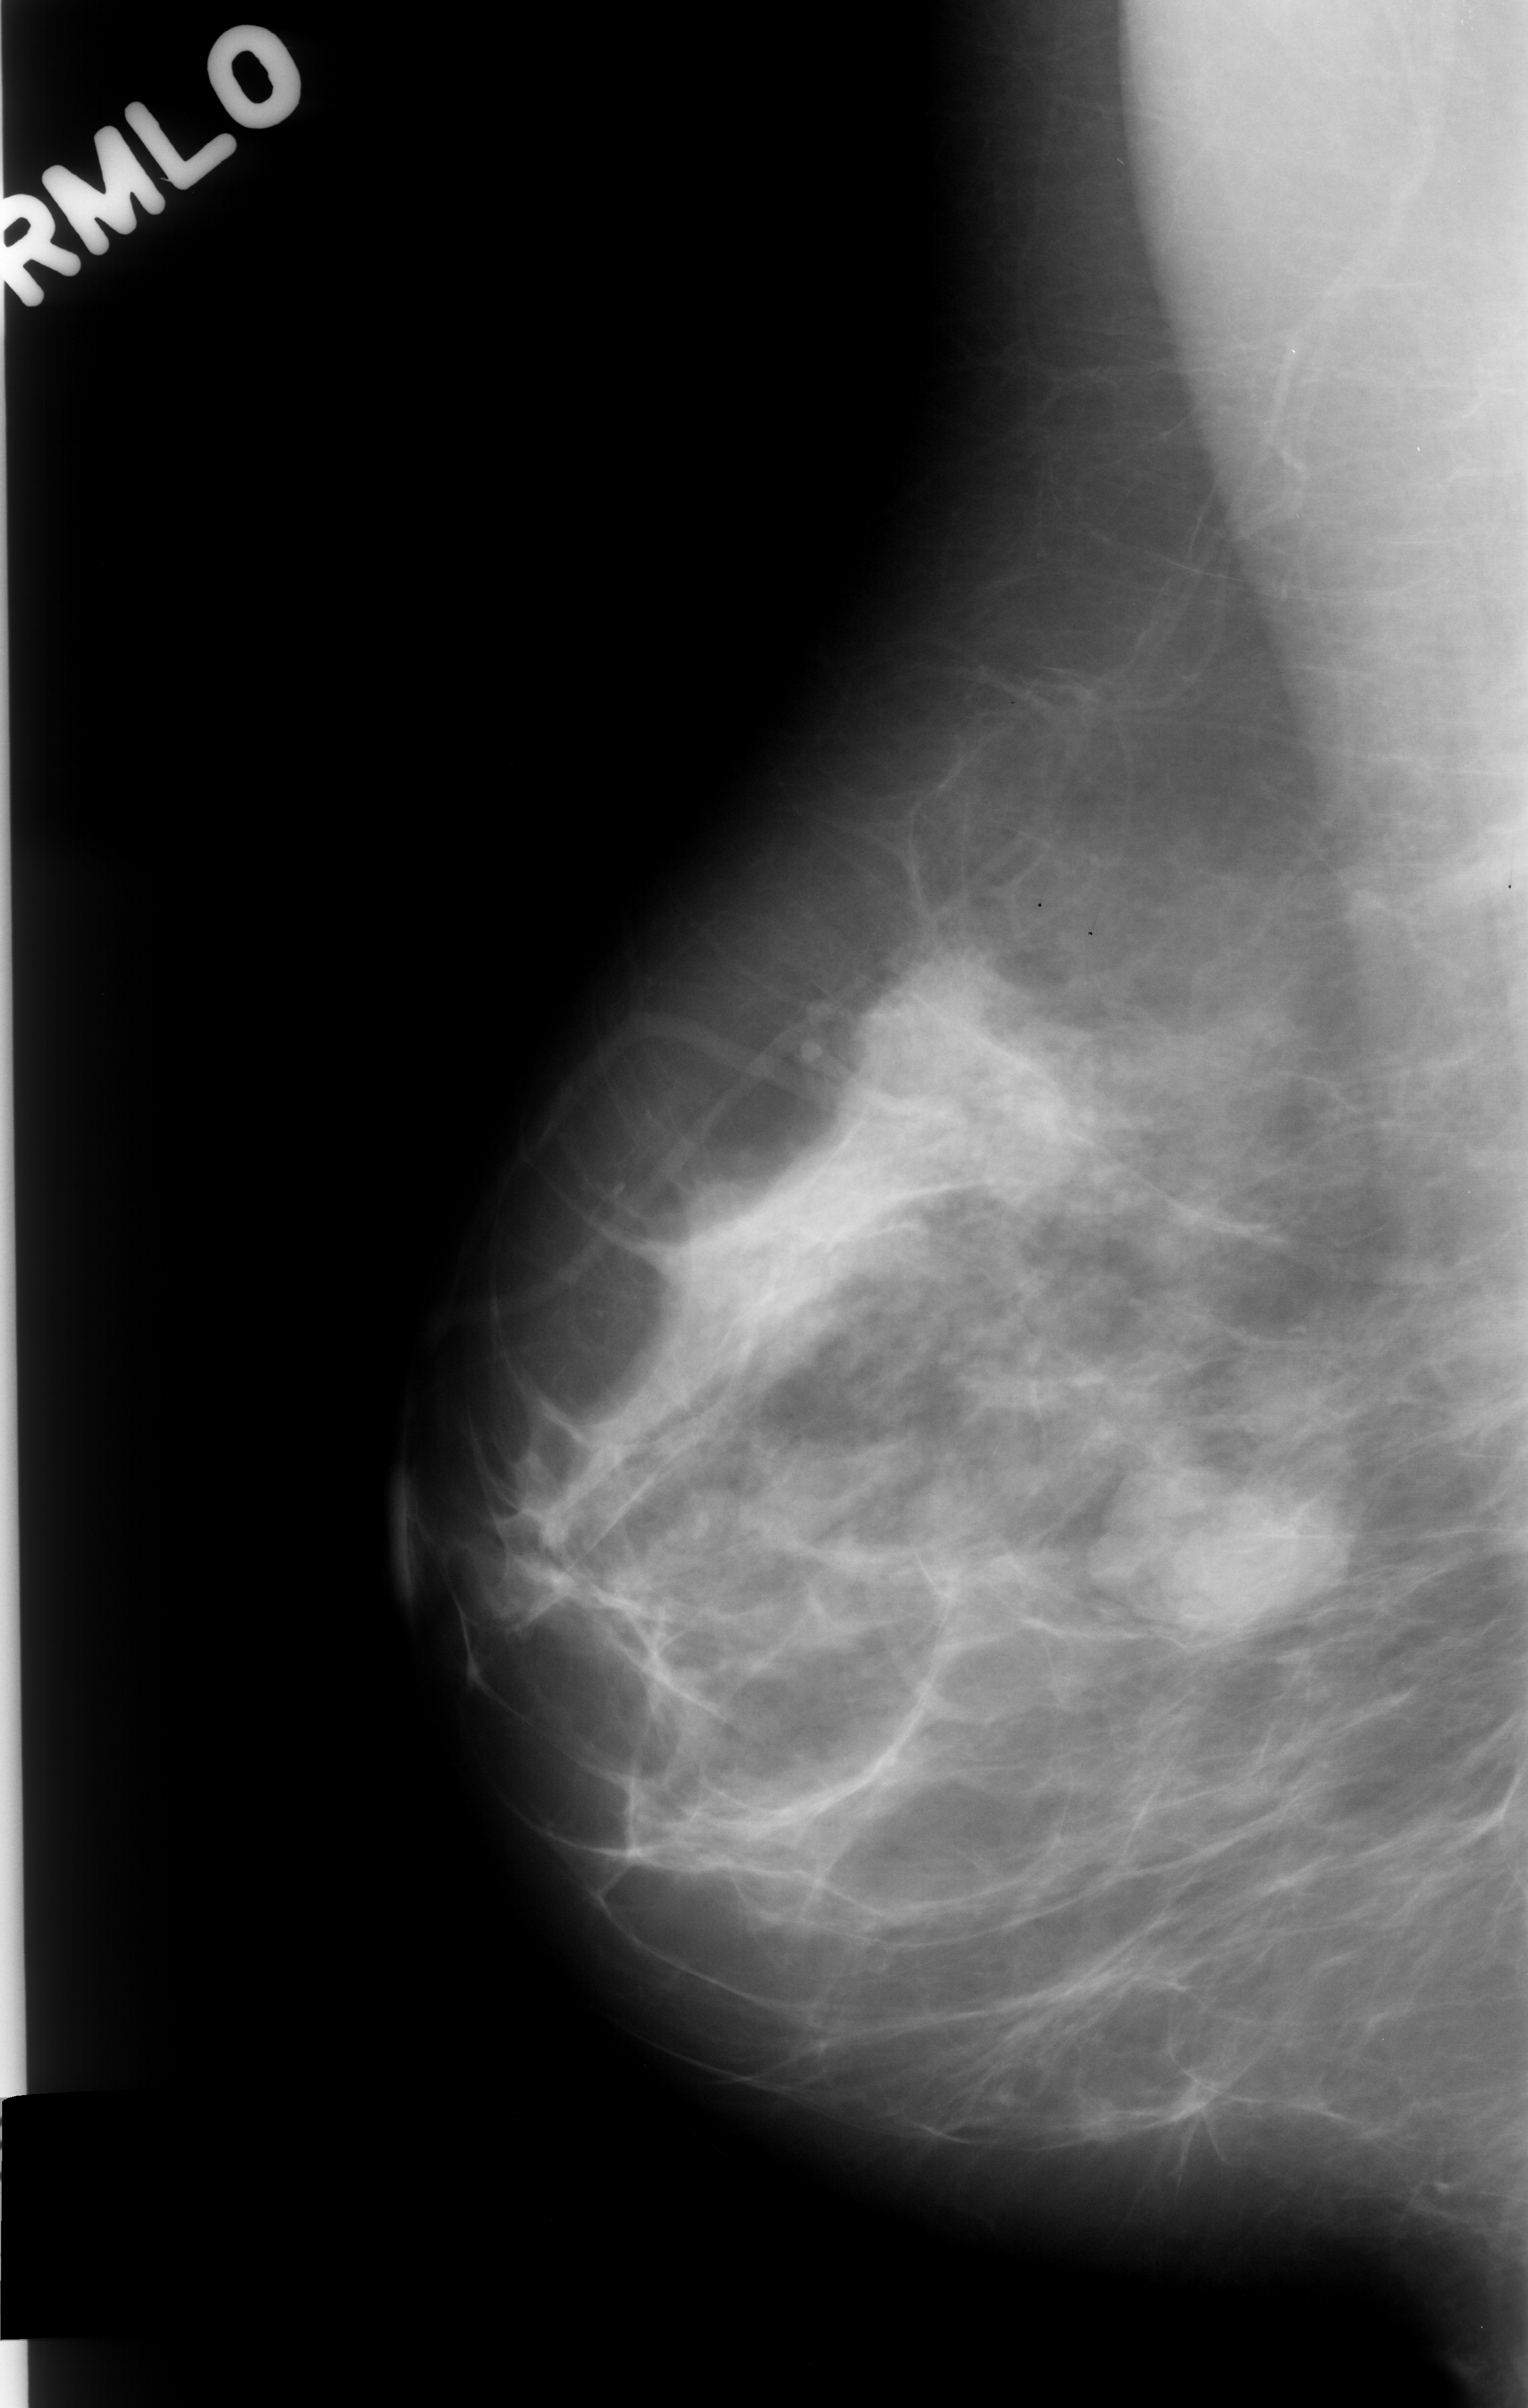
Digitized screen-film mammogram. Right breast. MLO view. Breast composition: scattered fibroglandular densities (BI-RADS density category 2 of 4). 1528 × 2408 image matrix.
Expert-marked regions of interest on this image (one box per marked abnormality):
- mass, shape lobulated, margins circumscribed; BI-RADS assessment category 4; pathology (as recorded): benign: bounding box (x1, y1, x2, y2) in pixels: (1161, 1478, 1359, 1661)